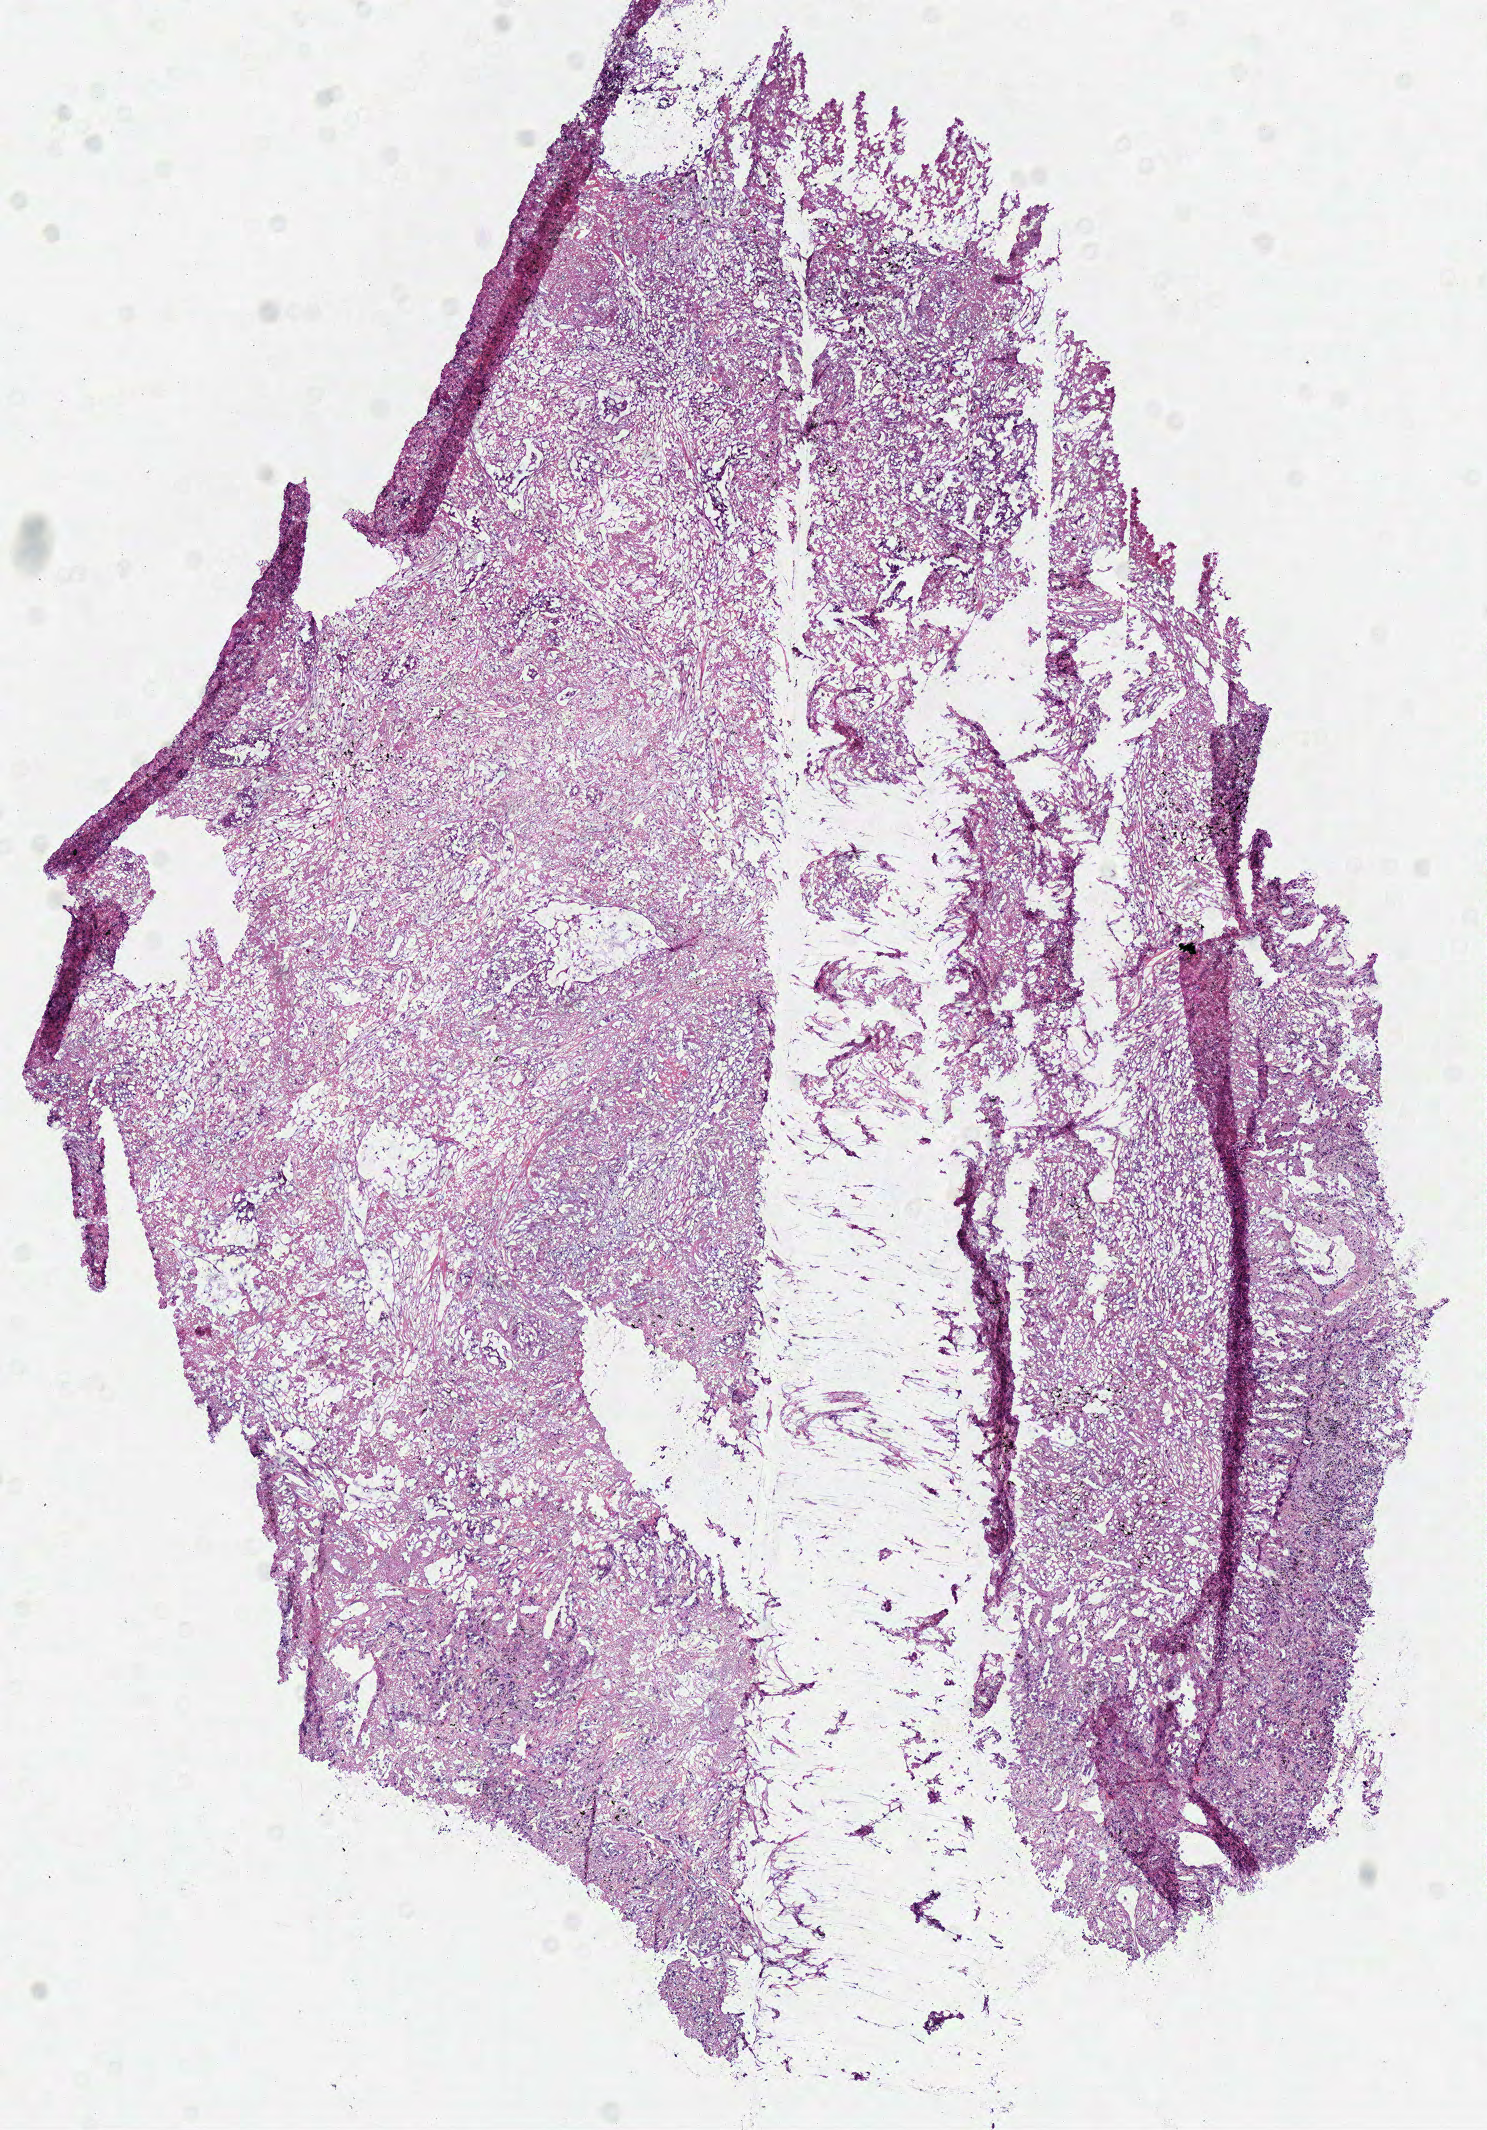
Digitized H&E tissue section (whole slide) — a low-resolution overview of the entire scanned area, about 5.9 x 8.4 mm (from a 40x scan); frozen section from the top of the tissue portion; sample: primary tumour, lung. Patient: female, age at initial diagnosis 74 years. Slide review estimates, as recorded: tumour cells 85%, tumour nuclei 75%, normal cells 0%, stromal cells 15%, necrosis 0%.
AJCC pathologic stage: IIIA. Laterality: right. Histologic diagnosis: Adenocarcinoma, NOS (upper lobe, lung).